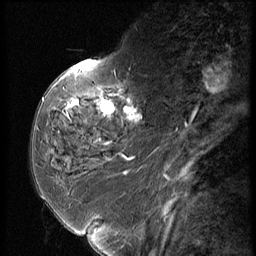
Breast MRI (dynamic contrast-enhanced), one sagittal slice; position 19 of 56 along the scan axis; dynamic contrast-enhanced series, image 2 of 3 at this slice position (ordered by acquisition); 1.5 T; TE 4.2 ms, TR 9 ms; 2.5 mm slice thickness; 256 × 256 image matrix, field of view 180 × 180 mm. Female patient, age 59 years. From the clinical record (not read from this slice): setting: breast cancer imaged before/during neoadjuvant chemotherapy; receptor status: HER2-positive.
Outlined on this slice (semi-automatically segmented with operator editing):
- analysis volume of interest (the breast-tissue region the enhancement analysis was run in; not a lesion): bounding box <44,66,151,135> (left, top, right, bottom; pixels)
- tumour enhancement mask (voxels above the 140 % enhancement threshold inside the analysis volume of interest): <67,98,137,120>